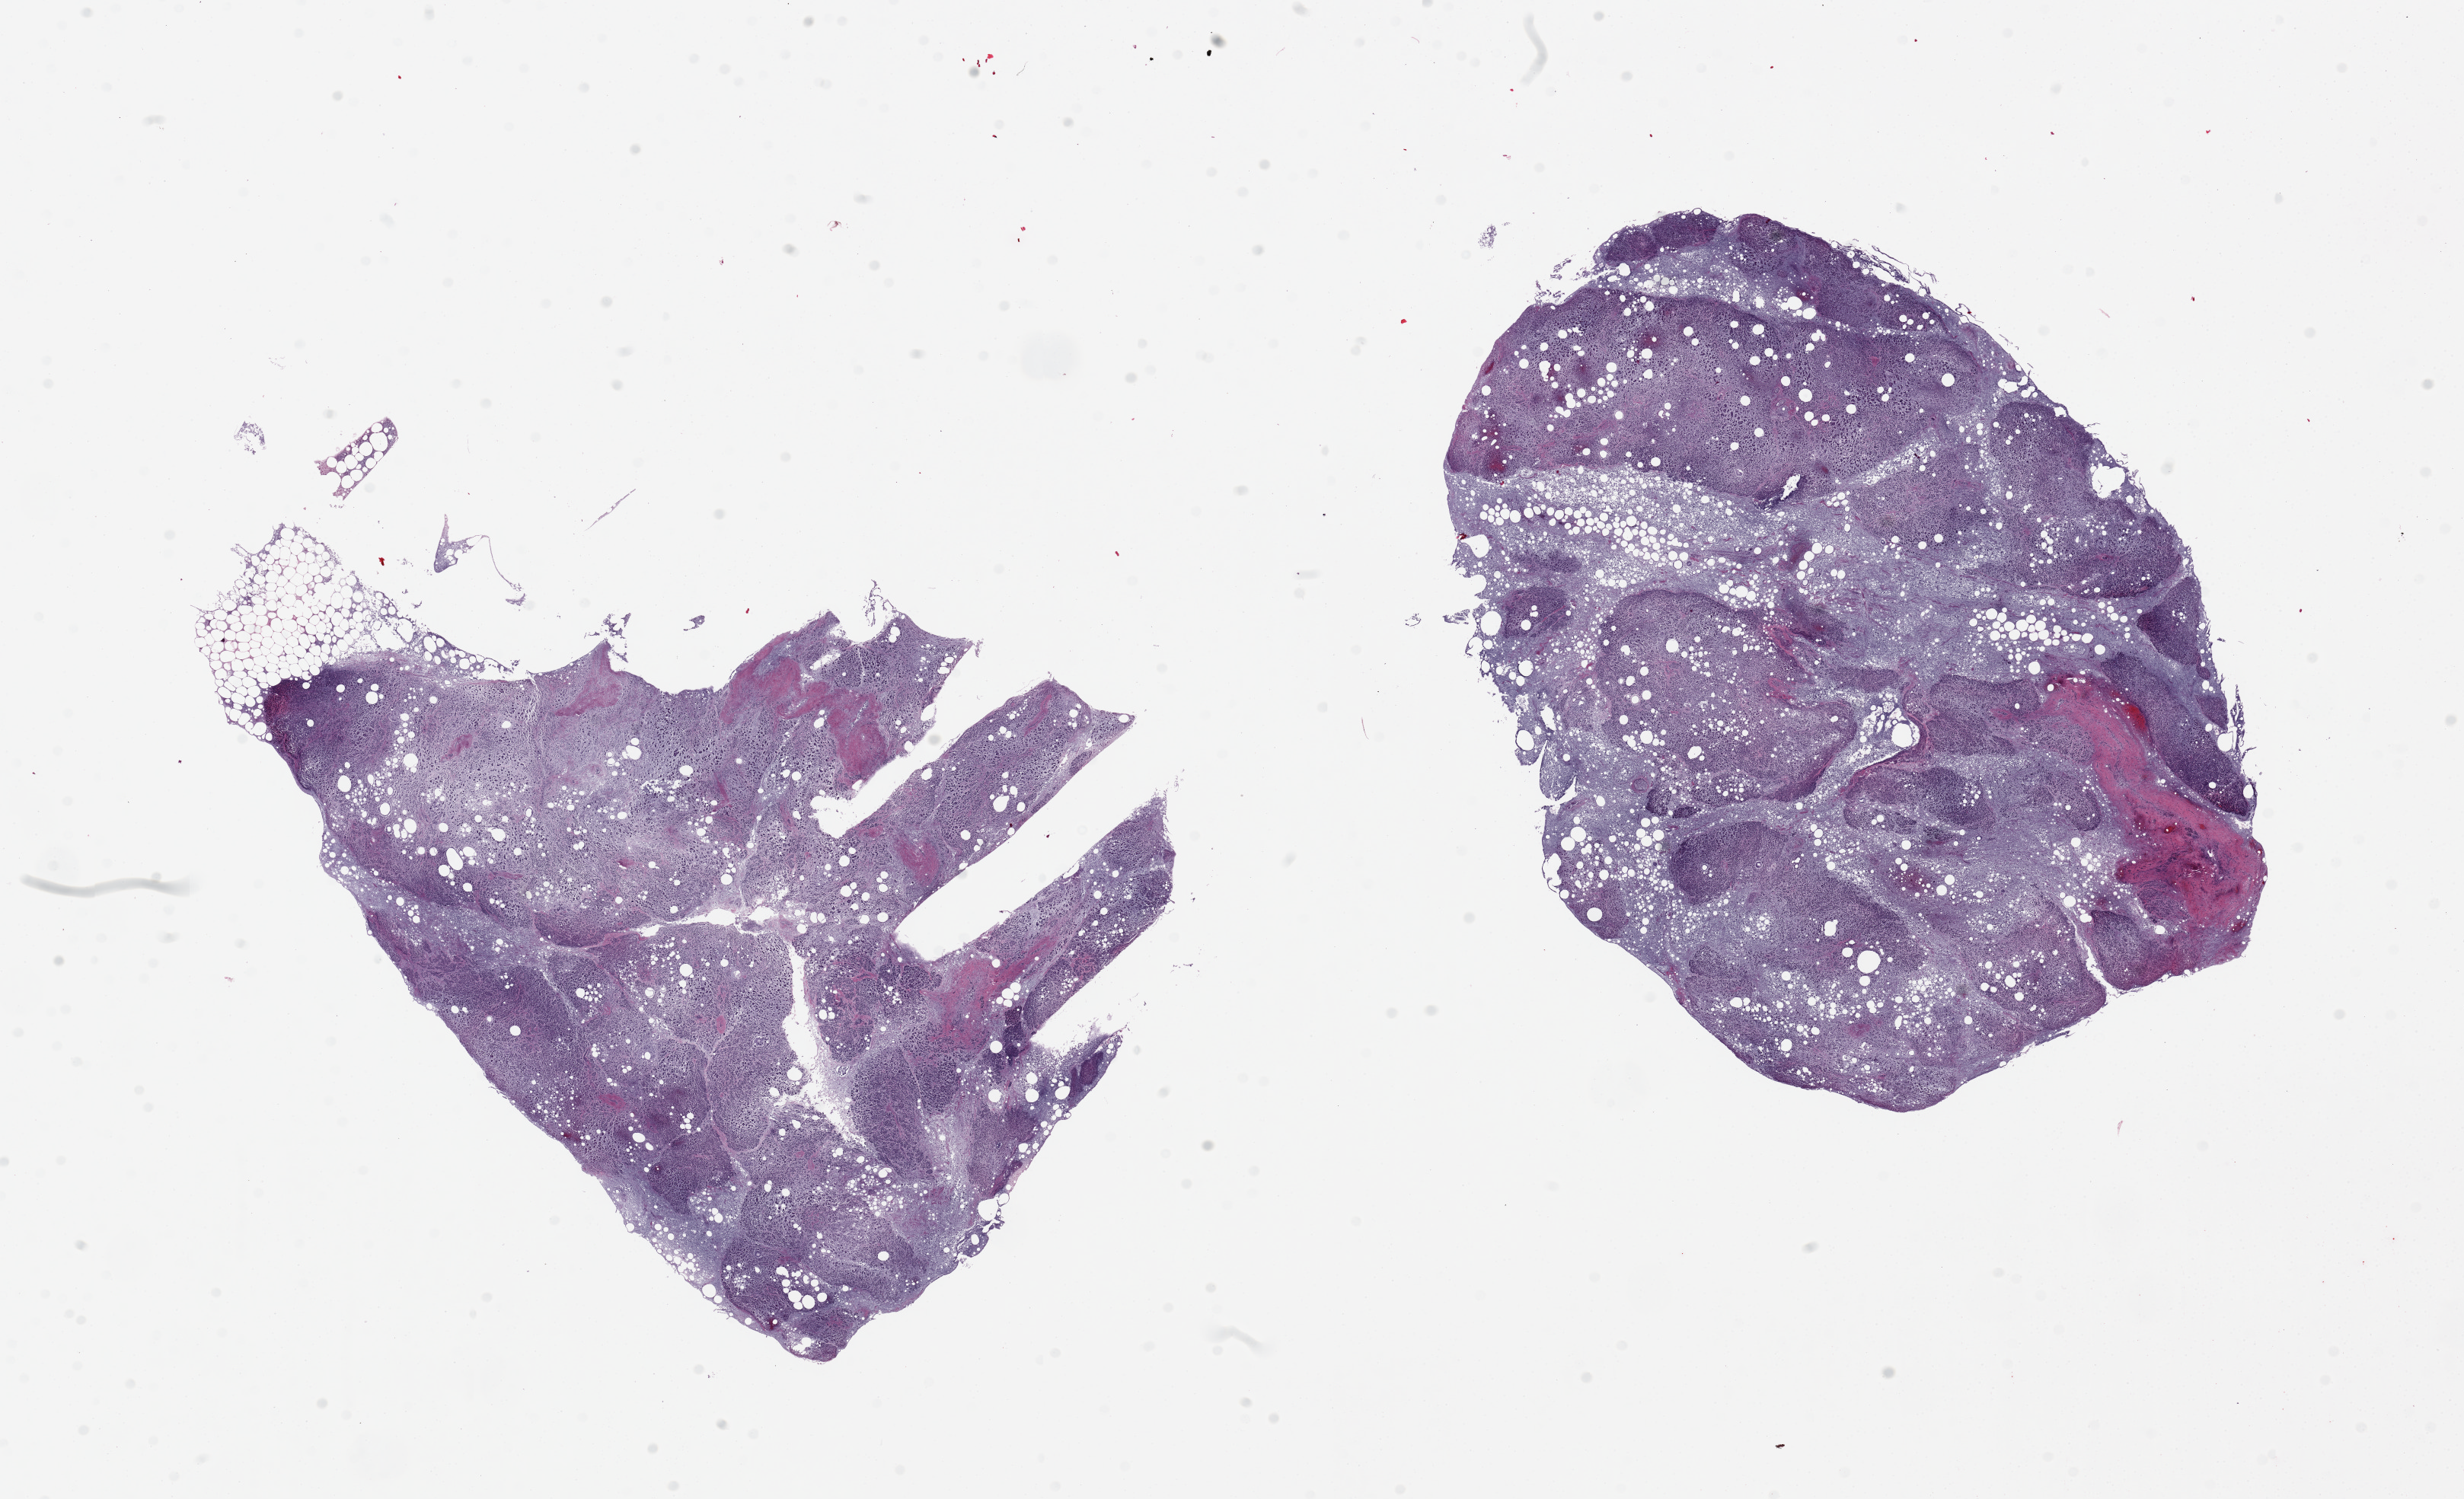
Hematoxylin and eosin (H&E) whole-slide image — a low-resolution overview of the entire scanned area, about 25.6 x 15.6 mm. PAXgene-fixed paraffin-embedded (PFPE) section. Sampled site (target tissue): pancreas. Donor tissue sample. Male donor.
Reviewer comment on this tissue sample: 2 pieces, extreme autolysis/saponification.